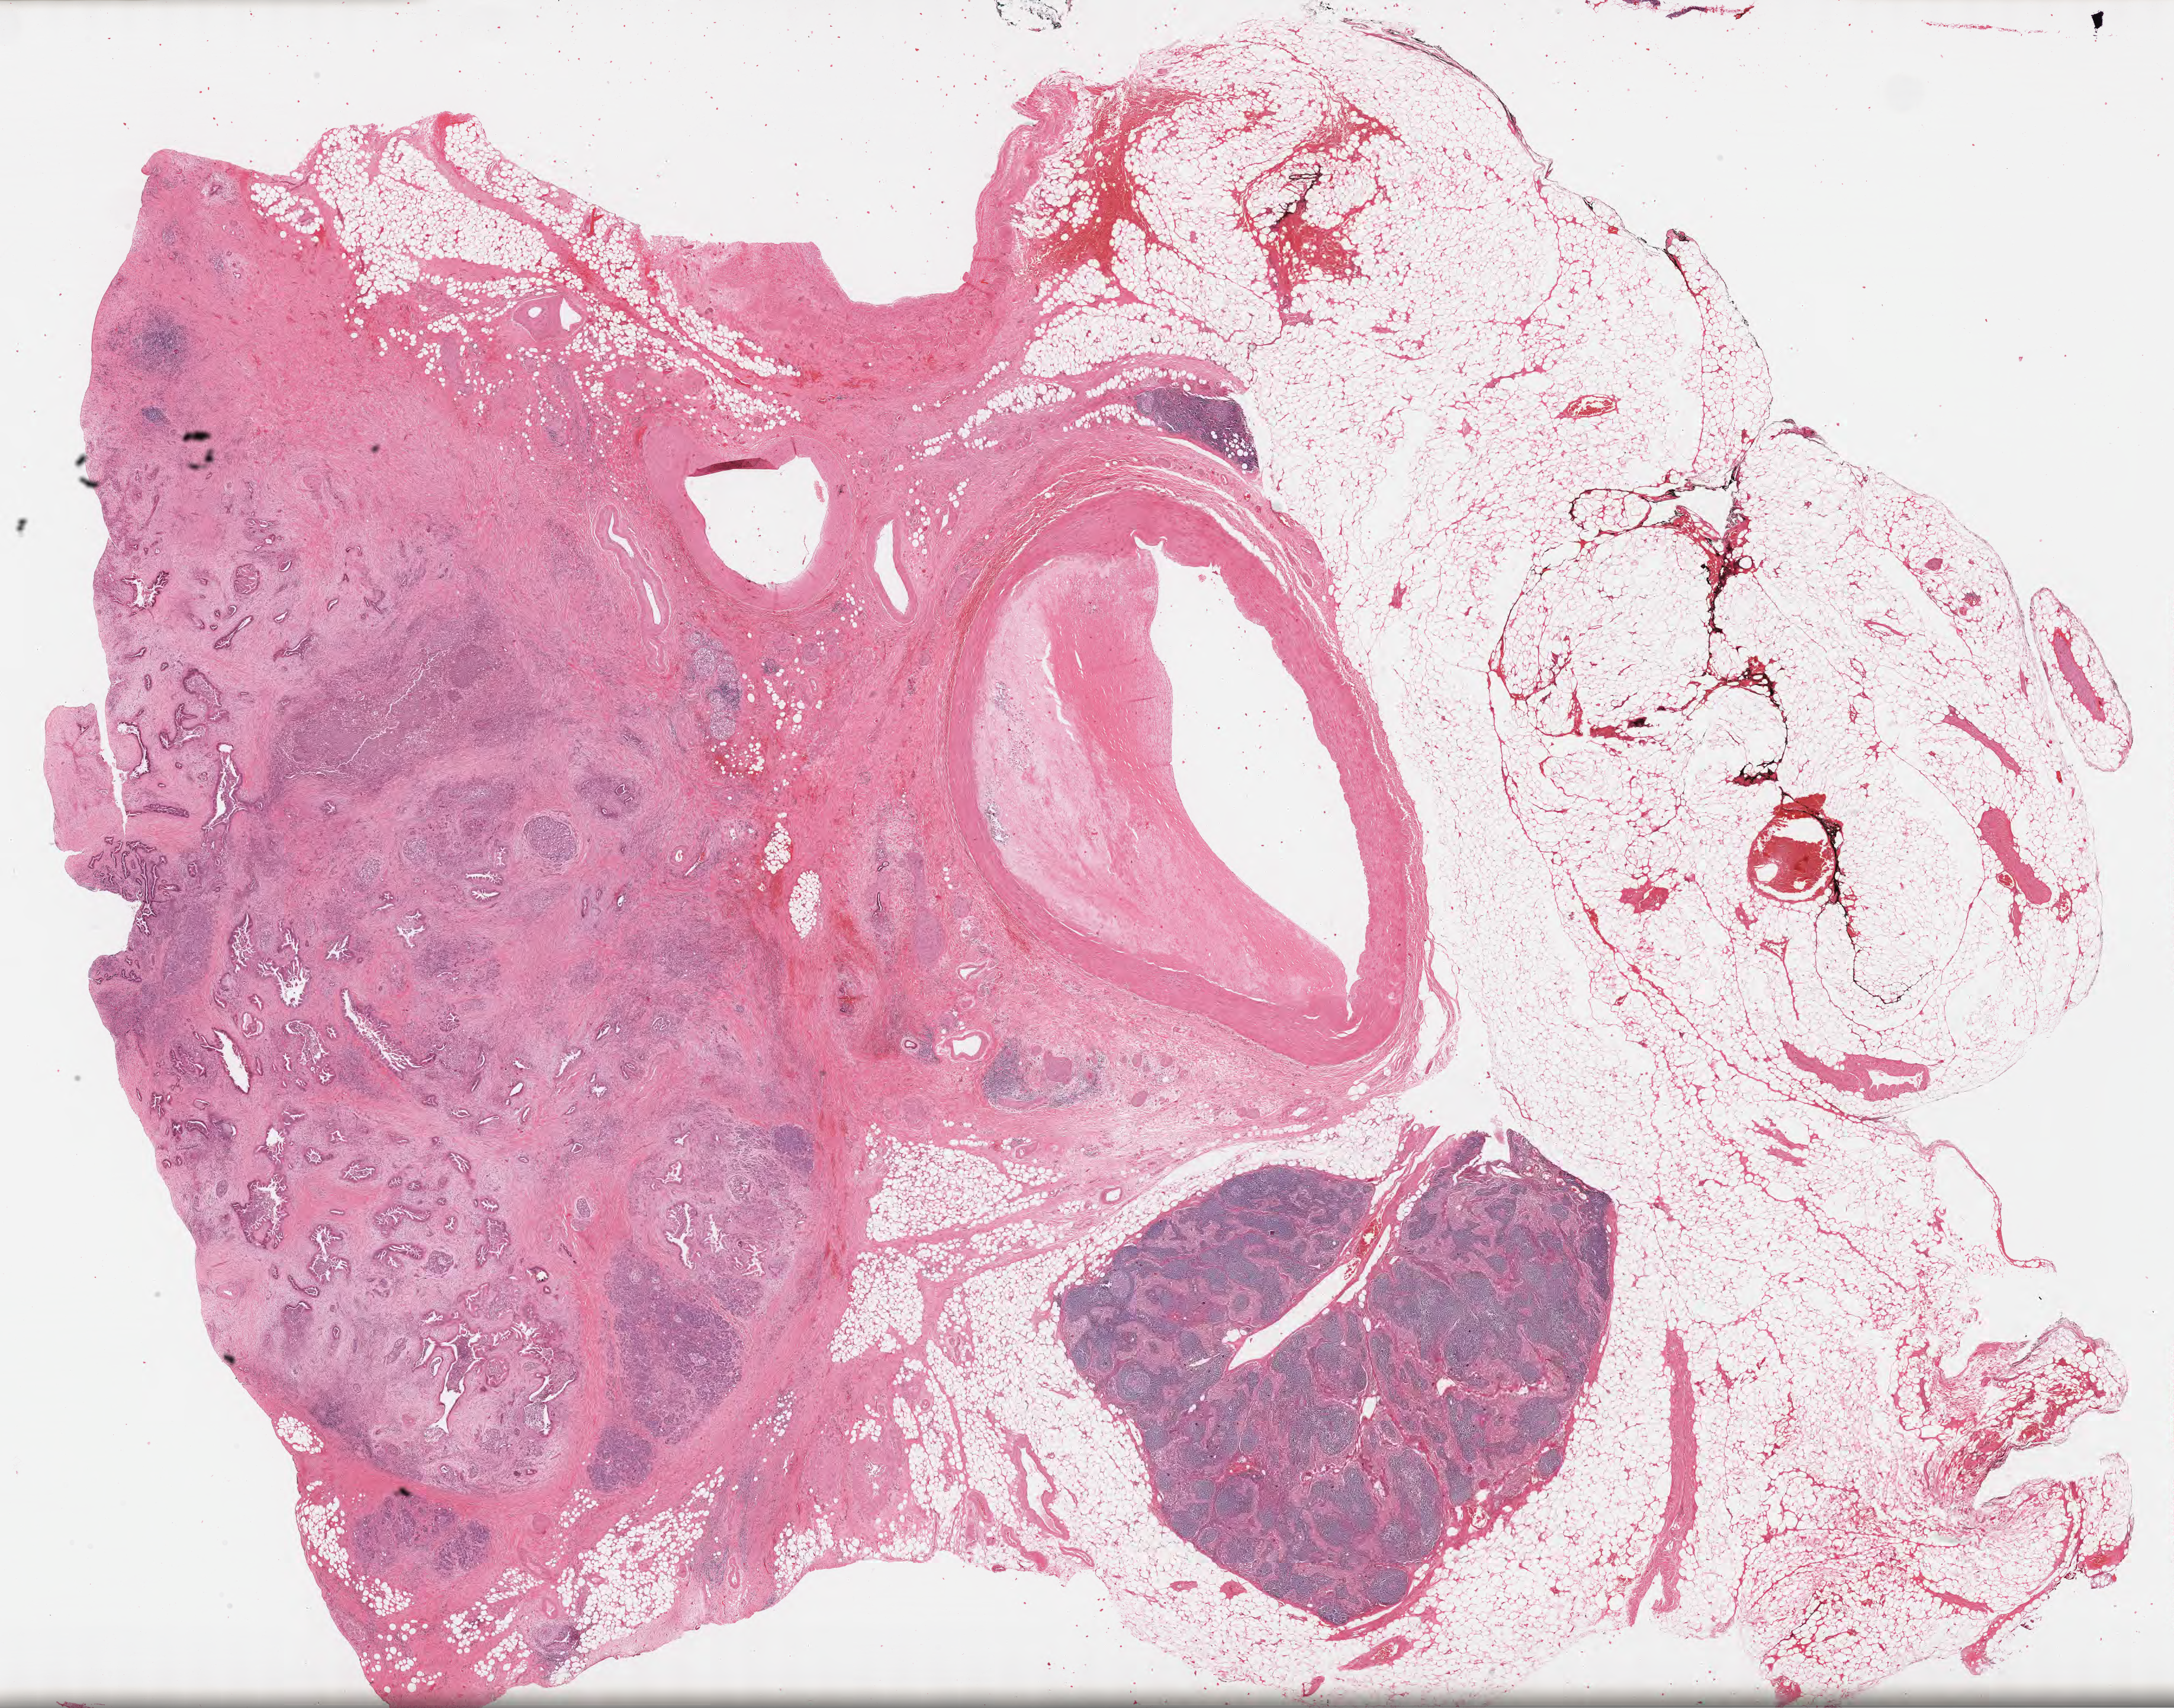
Whole-slide image, hematoxylin and eosin (H&E) stain, shown as a low-resolution overview of the whole scanned area (about 29.7 x 23.3 mm); formalin-fixed, paraffin-embedded (FFPE) tissue; primary tumor; site: body of pancreas. Male, age 80 years at initial diagnosis. Tumor grade: G1 (well differentiated). Pathologist review of this section (percent, as recorded): tumor cells 35%, tumor nuclei 35%, stromal cells 60%, necrosis 0%, normal cells 5%. Infiltration values recorded for this section: lymphocyte infiltration 15%, monocyte infiltration 6%, neutrophil infiltration 20%.
Section: bottom of the tissue portion. Diagnosis: Adenocarcinoma, NOS.